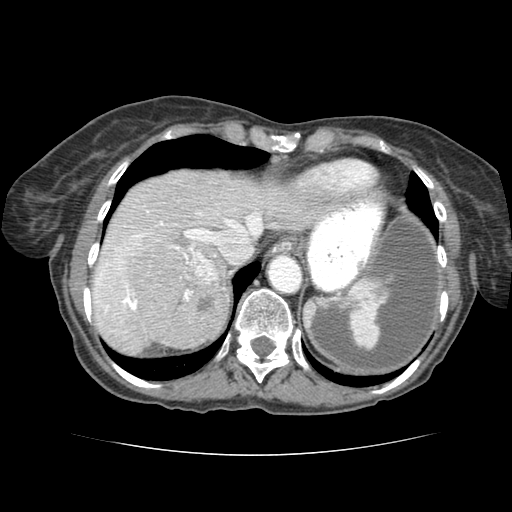
Contrast-enhanced abdominal CT (liver protocol), one axial slice. Position 66 of 77 along the scan axis. Reconstruction kernel STANDARD. 120 kVp. Soft-tissue window (W 400 / L 40 HU). 512 × 512 image matrix. From the clinical record (not read from this slice): diagnosis: hepatocellular carcinoma (patient treated with transarterial chemoembolisation; whether this scan precedes or follows treatment is not stated here); TNM stage (as recorded): Stage-I; Child-Pugh class: A; tumour differentiation: well differentiated; tumour nodularity: uninodular.
Structures marked on this image (semi-automatic segmentation, software-assisted and operator-edited):
- abdominal aorta: box from (x=268, y=254) to (x=300, y=292) px
- liver parenchyma outside the tumour (the mass and vessels are separate outlines, so this box may not span the whole liver): (x=90, y=168)–(x=312, y=346)
- mass: (x=130, y=246)–(x=224, y=342)
- liver vessels: (x=118, y=221)–(x=226, y=307)